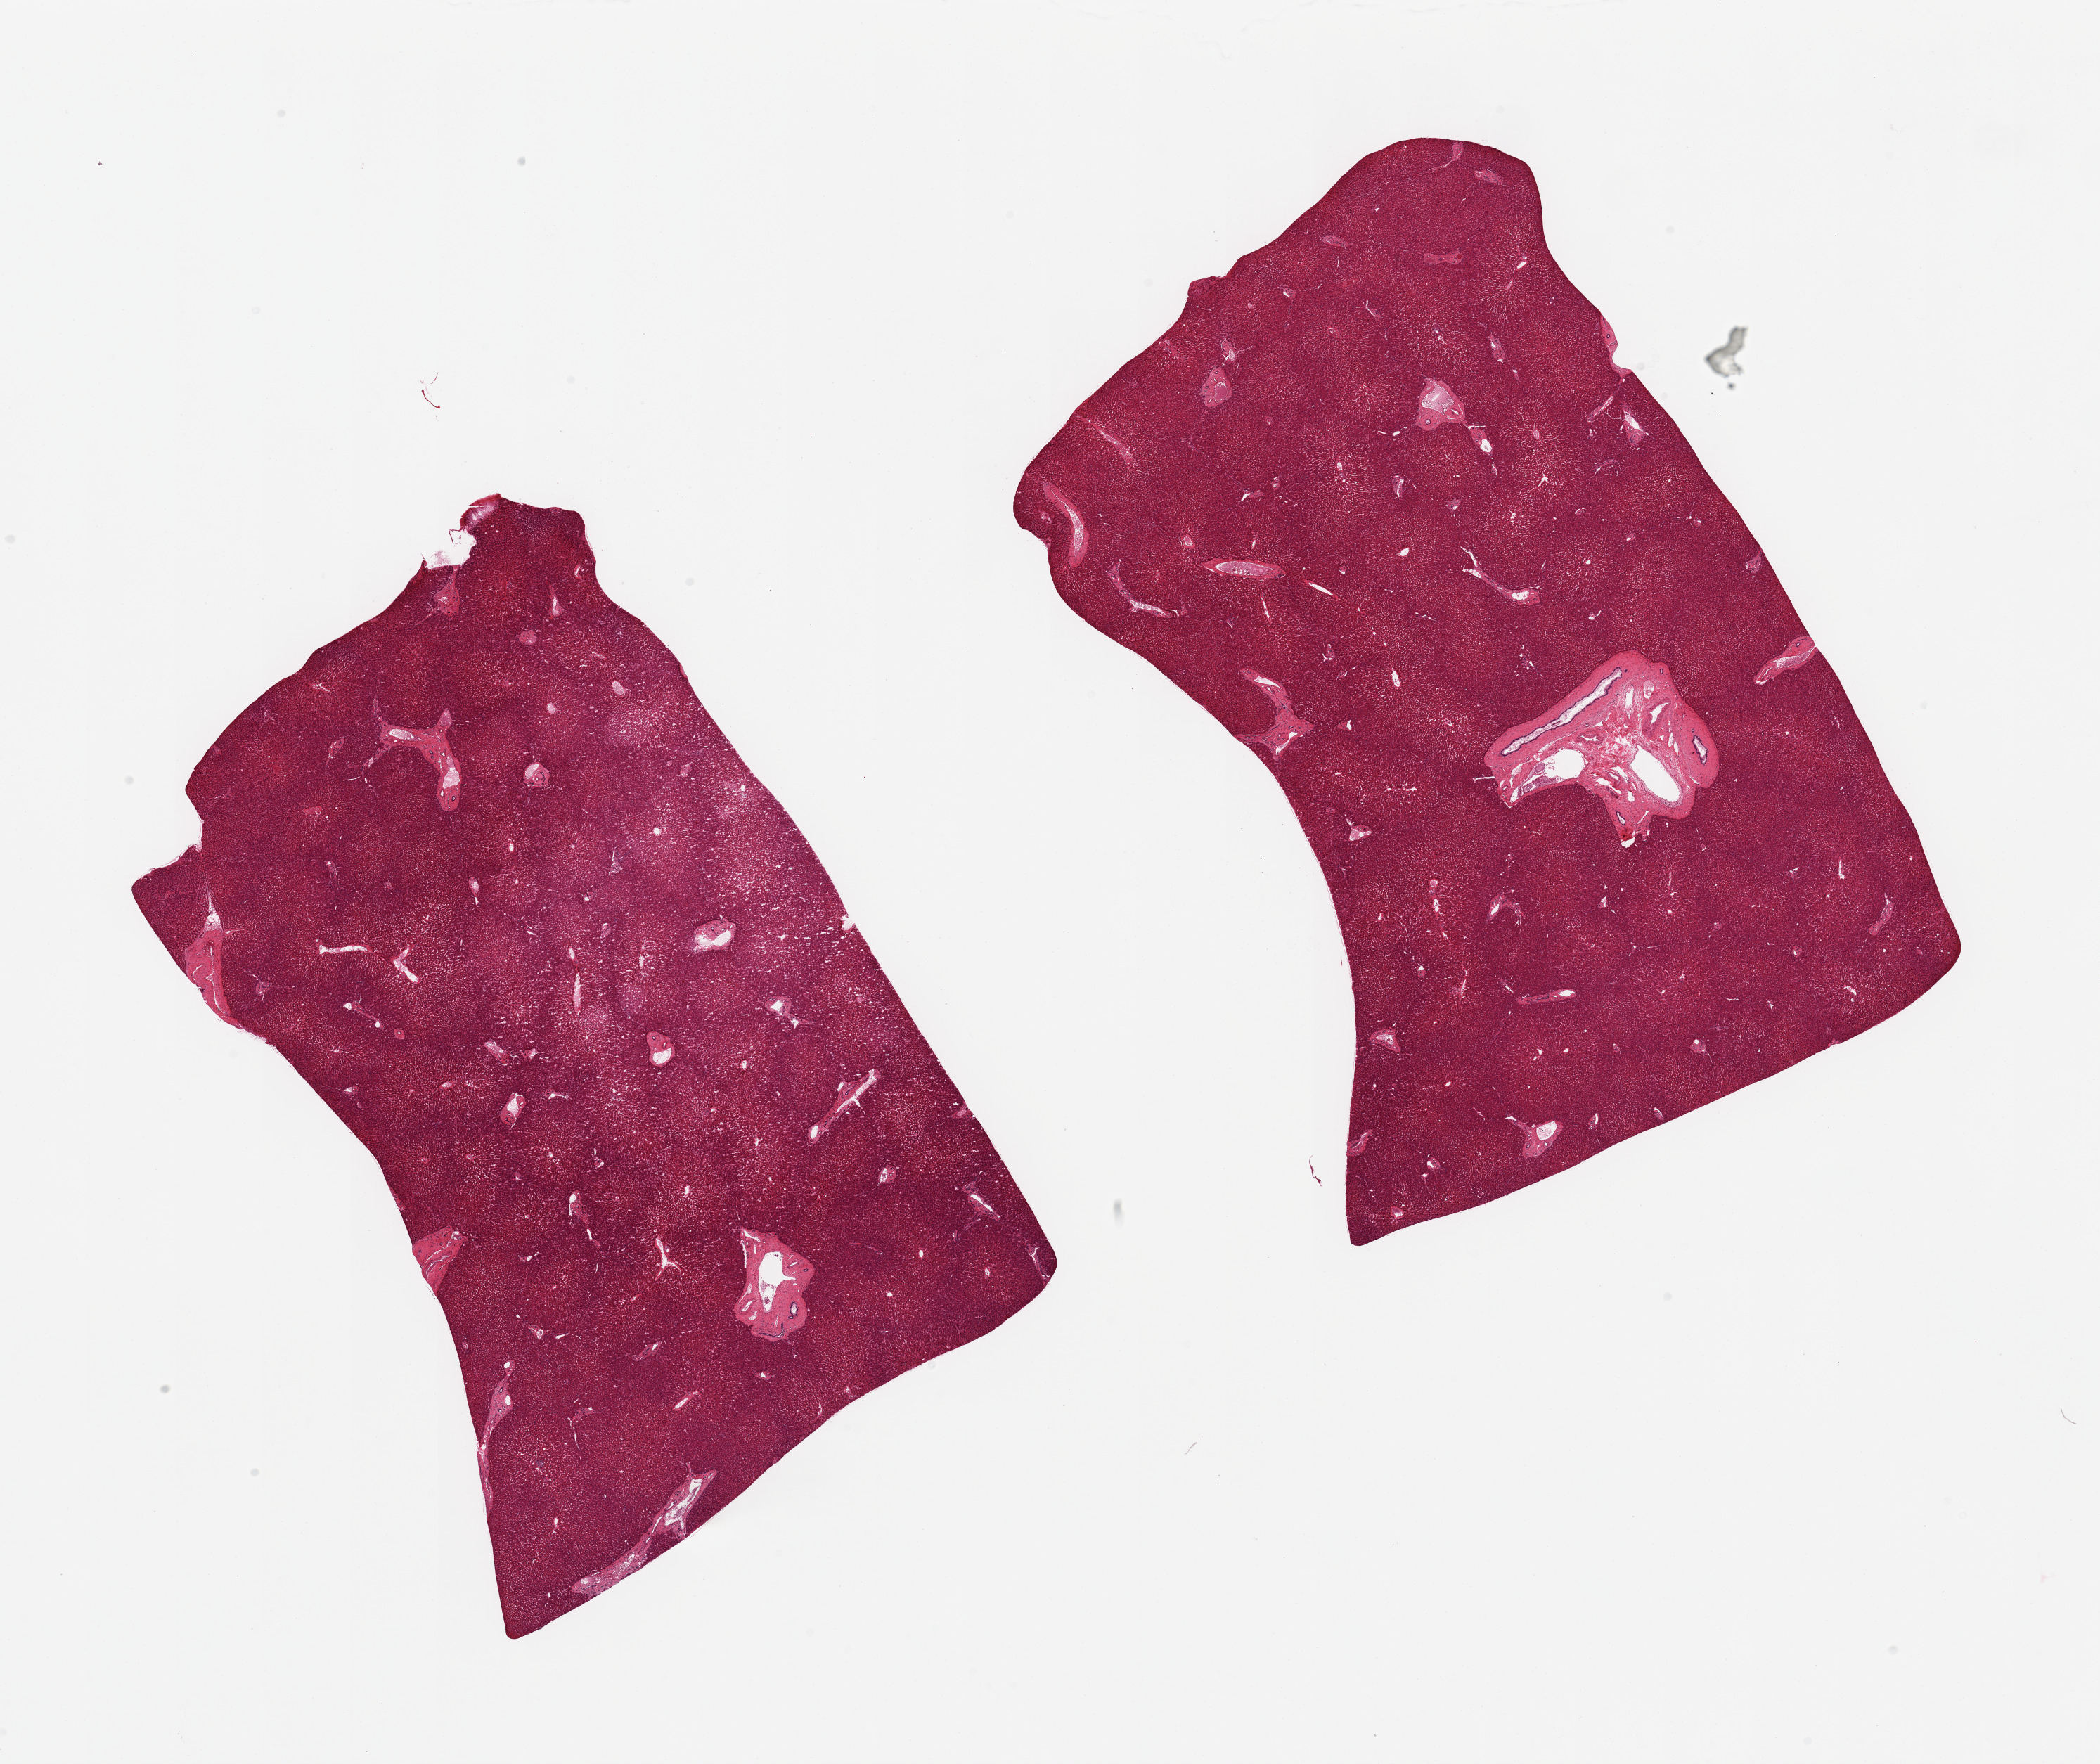
Whole-slide image, haematoxylin and eosin stain, a low-resolution overview of the entire scanned area, about 23.6 x 19.8 mm (slide scanned at 20x), PAXgene-fixed, paraffin-embedded tissue, section of liver (target tissue), tissue donor sample.
Pathologist's review note for this sample: 2 pieces.